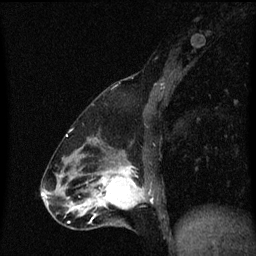
Breast MRI (dynamic contrast-enhanced), one sagittal slice; slice 26 of 60 in the series (ordered by position); dynamic contrast-enhanced series, image 2 of 3 at this slice position (ordered by acquisition); 1.5 T; TE 4.2 ms, TR 8.4 ms; 256 × 256 image matrix, field of view 200 × 200 mm. Female patient, age 47 years.
Annotated regions visible in this slice (semi-automatically segmented with operator editing):
- analysis volume of interest (the breast-tissue region the enhancement analysis was run in; not a lesion): bounding box (x1, y1, x2, y2) in pixels: (100, 172, 151, 209)
- tumour enhancement mask (voxels above the 70 % enhancement threshold inside the analysis volume of interest): (100, 172, 146, 209)